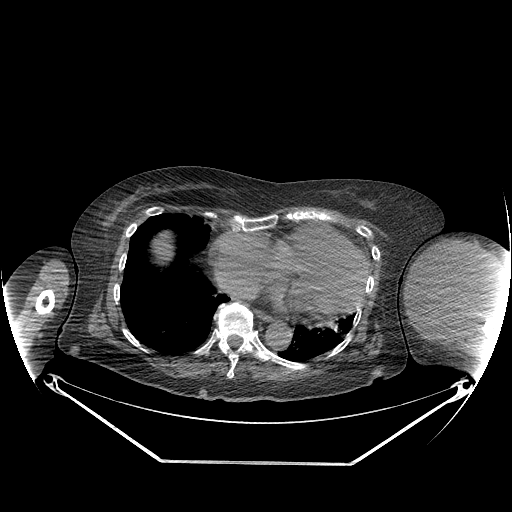
CT of an extremity soft-tissue mass (from a PET/CT study), one axial slice; reconstruction kernel STANDARD; 140 kVp; soft-tissue window (W 400 / L 40 HU); 3.75 mm slice thickness; 512 × 512 image matrix. Female patient. From the clinical record (not read from this slice): histological type: pleiomorphic leiomyosarcoma; grade: high; site of the primary tumour: left biceps.
Annotated regions visible in this slice (expert contour drawn on MRI and transferred to this co-registered scan by the dataset authors):
- gross tumour volume including surrounding oedema: bounding box [x1, y1, x2, y2] px = [406, 240, 497, 330]
- gross tumour volume (mass): [406, 240, 497, 328]